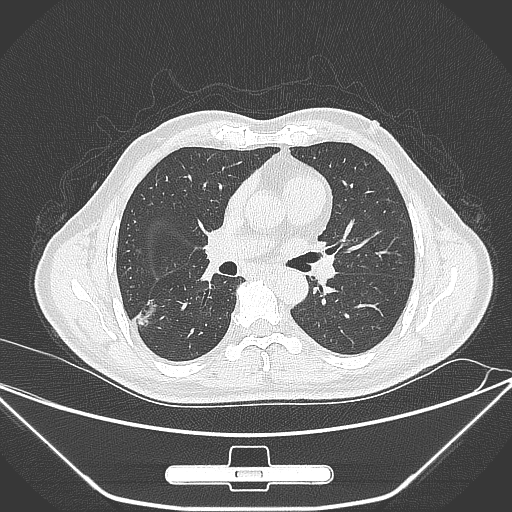
Chest CT, one axial slice. Slice 157 of 310 in the series (ordered by position). Lung window (W 1500 / L -600 HU). 512 × 512 image matrix, field of view 398 × 398 mm. Male patient, age 71 years. Case-level facts recorded for this patient, not image findings: clinical TNM (as recorded): T1c N0 M0.
Structures marked on this image (bounding box drawn by a radiologist):
- lung tumour (recorded histology: adenocarcinoma): bounding box [x1, y1, x2, y2] px = [137, 295, 166, 337]